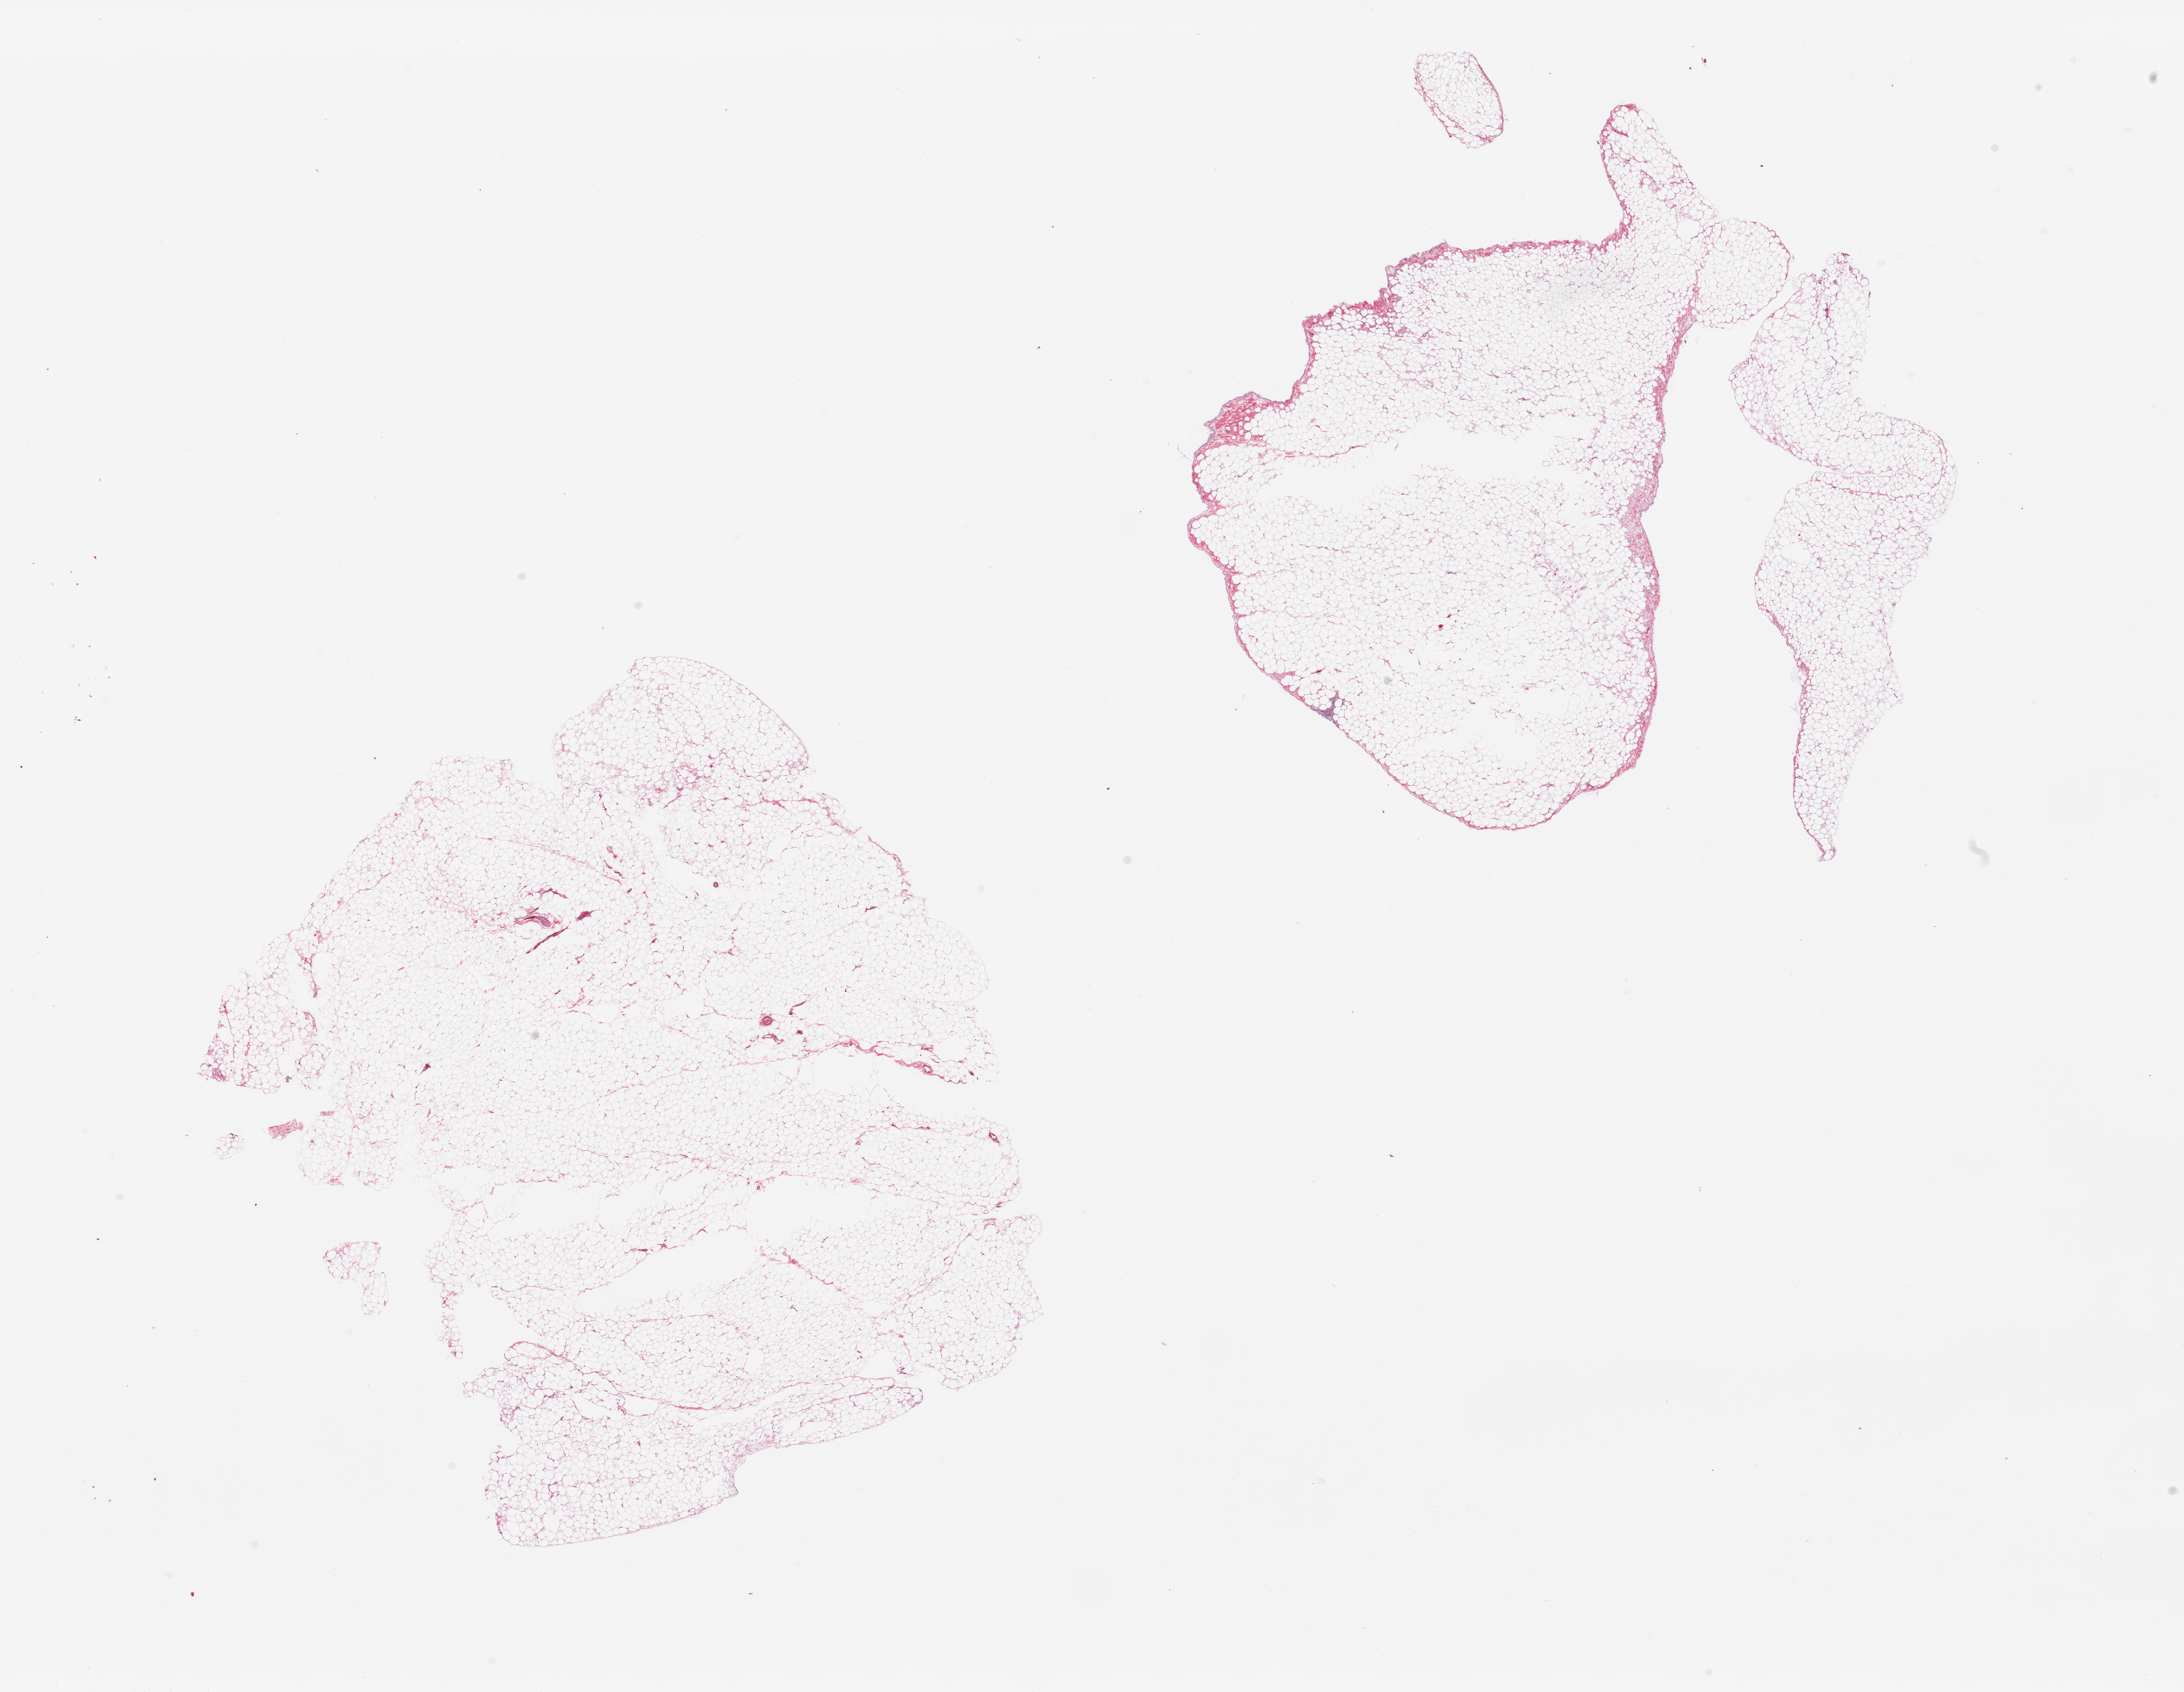
Digitized haematoxylin and eosin-stained section, brightfield — shown as a low-resolution overview of the whole scanned area (about 29.5 x 22.9 mm). PAXgene-fixed, paraffin-embedded tissue. Target tissue: omentum. Donor tissue sample.
Review note (as recorded): 2 pieces, small central defects (? poor fixation).